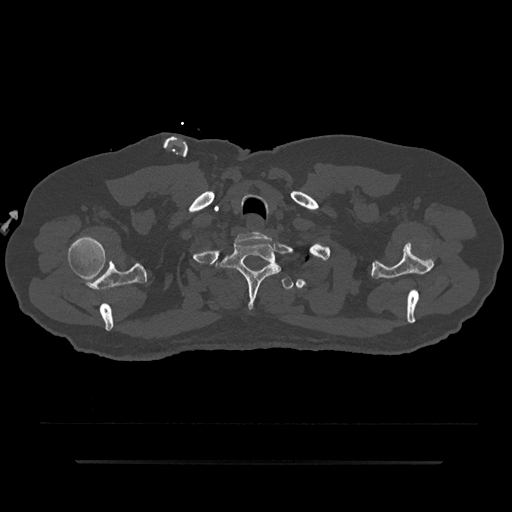
CT including the spine, one axial slice; position 735 of 797 along the scan axis; bone window (W 1800 / L 400 HU); 0.5 mm slice thickness; 512 × 512 image matrix, field of view 464 × 464 mm. Patient: male, 59 years. Case-level facts recorded for this patient, not image findings: primary cancer: bile ducts; vertebrae with lytic lesions (as recorded): T10.
Structures marked on this image (semi-automatically segmented with operator editing):
- T1 vertebra: box from (x=216, y=239) to (x=281, y=309) px
- T2 vertebra: (x=281, y=277)–(x=294, y=290)